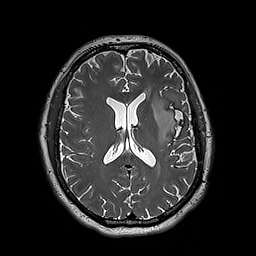
Brain MRI from a brain-tumour surgery series, one axial slice; position 91 of 192 along the scan axis; 256 × 256 image matrix, field of view 250 × 250 mm. Case-level facts recorded for this patient, not image findings: histopathology: Astrocytoma; WHO grade: 3; IDH mutation: yes.
Outlined on this slice (outlined manually by an expert reader):
- tumour: box from (x=152, y=95) to (x=179, y=144) px